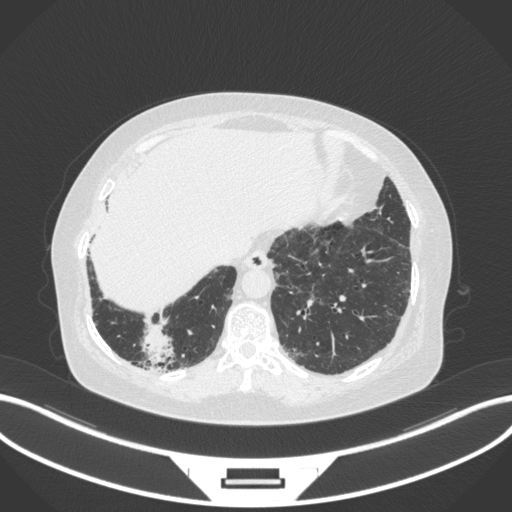
Chest CT, one axial slice; position 28 of 303 along the scan axis; reconstruction kernel B31f; lung window (W 1500 / L -600 HU); 1 mm slice thickness; 512 × 512 image matrix. Female patient, age 65 years. From the clinical record (not read from this slice): clinical TNM (as recorded): T2b N1 M0; histopathological grade: G1.
Outlined on this slice (bounding box drawn by a radiologist):
- lung tumour (recorded histology: adenocarcinoma): bounding box (x1, y1, x2, y2) in pixels: (137, 324, 181, 369)